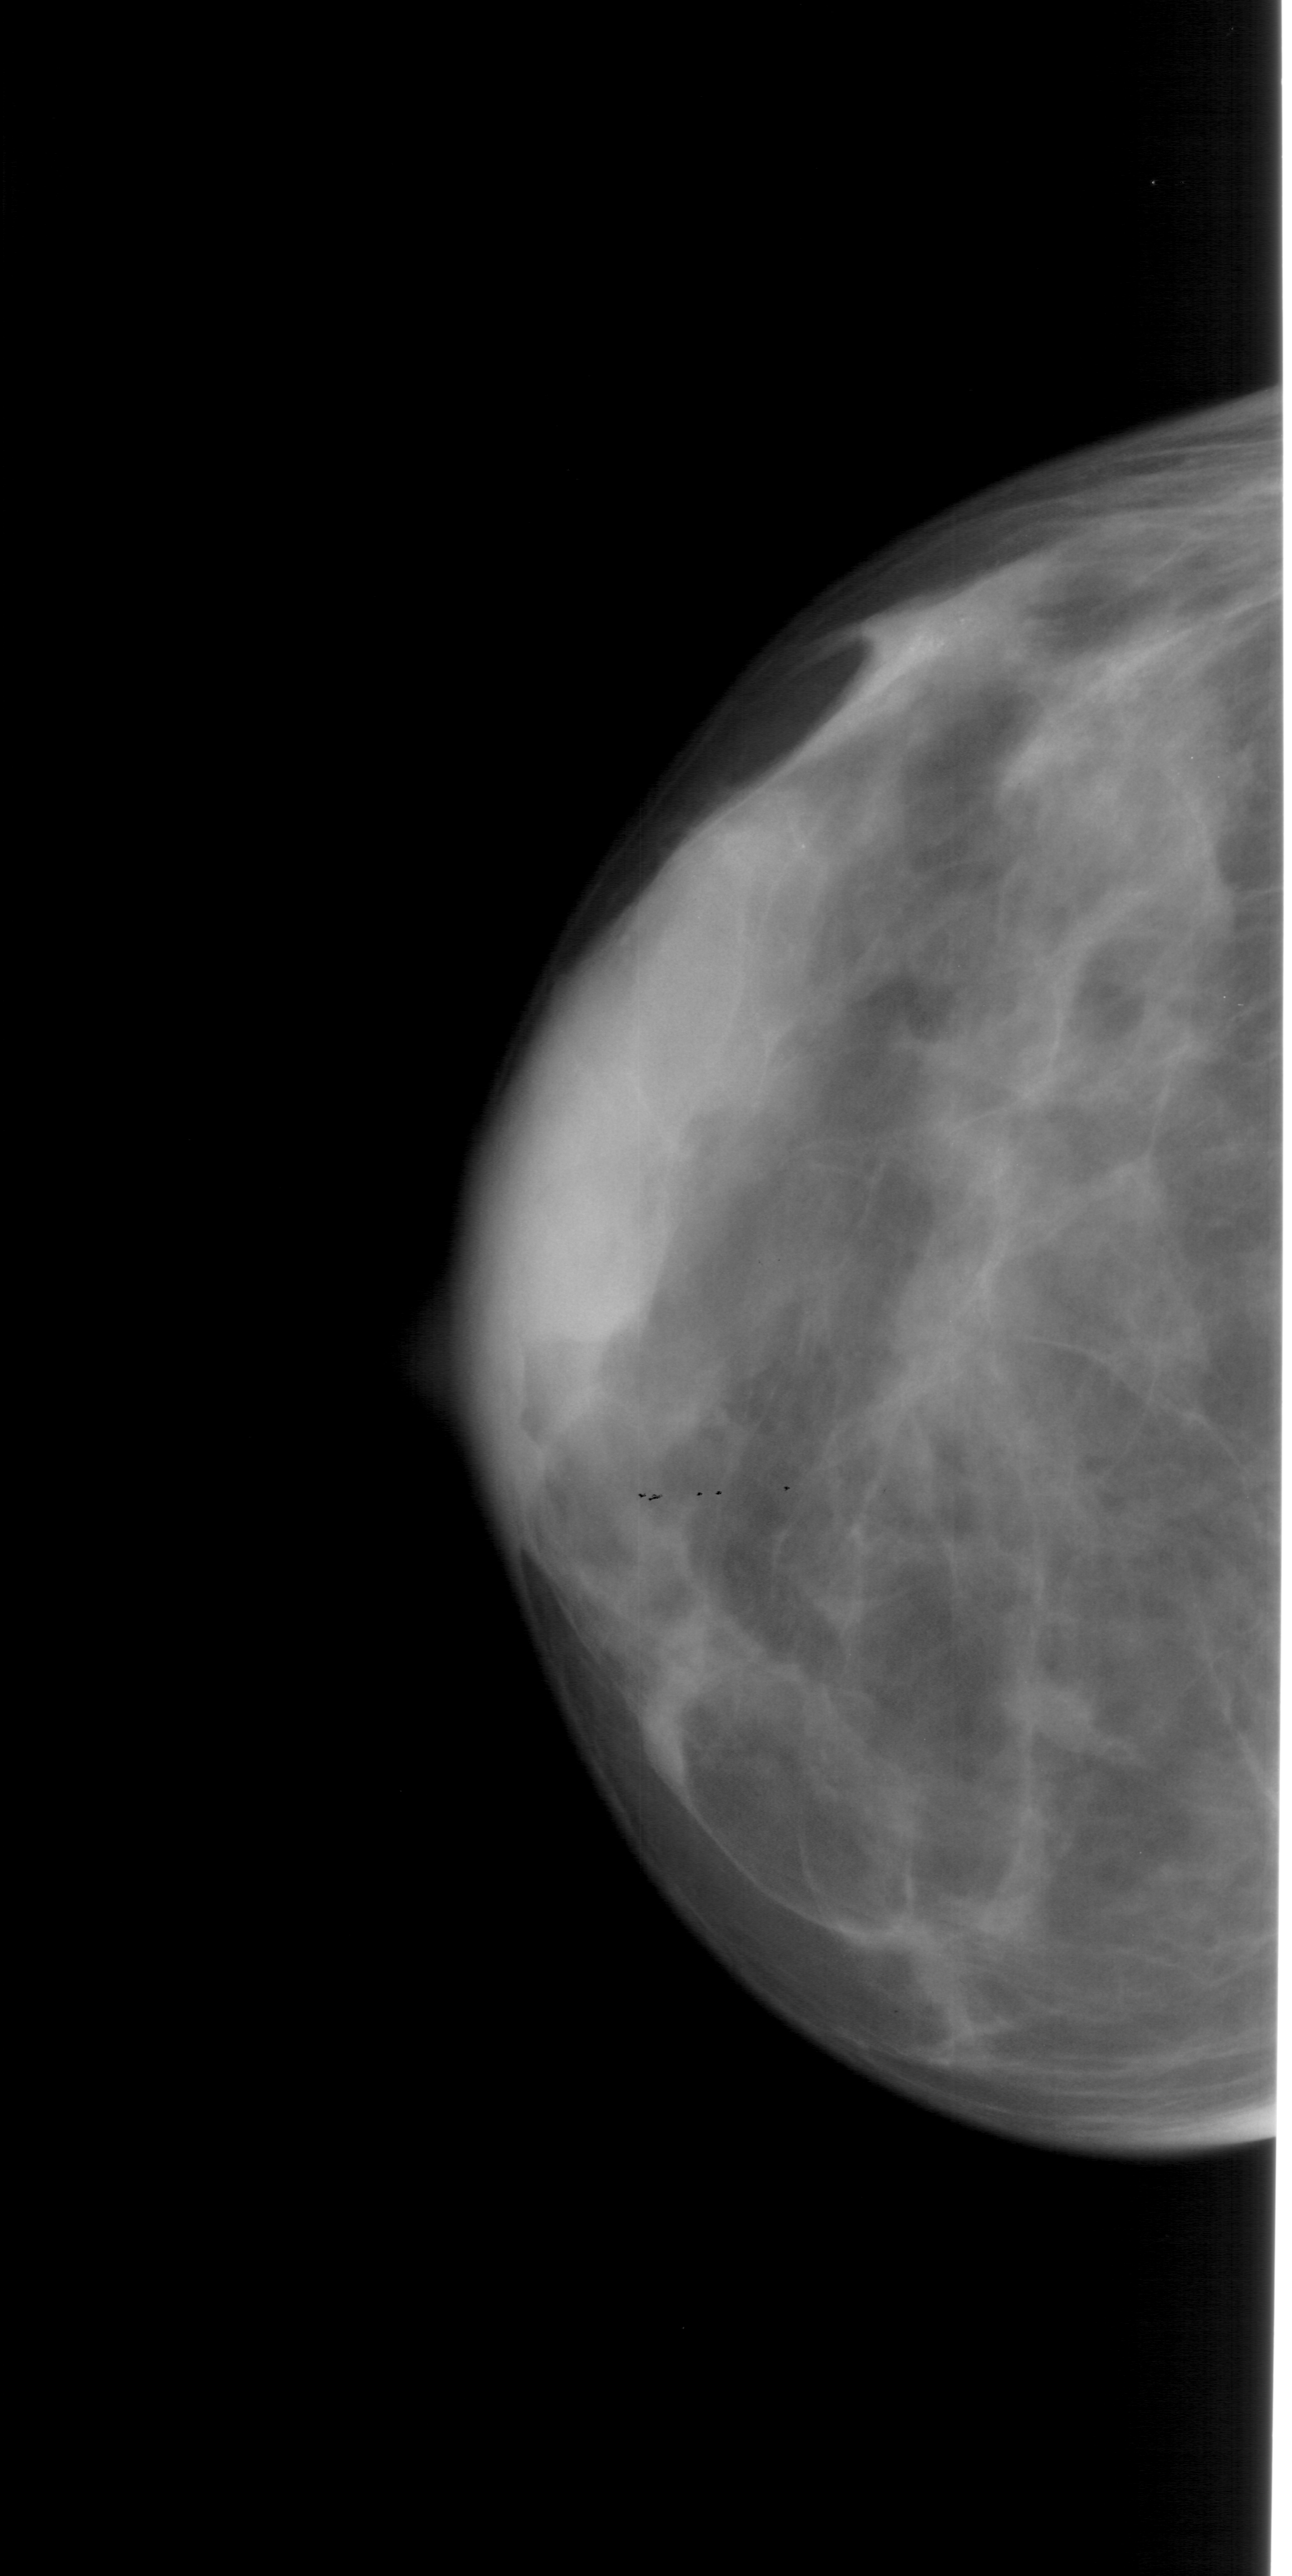
Scanned film-screen mammogram, left breast, craniocaudal (CC) view, BI-RADS breast density category 4 (scale 1–4).
Calcifications, morphology pleomorphic, distribution clustered; BI-RADS assessment category 4; subtlety rating 1 on a 1 (subtle) to 5 (obvious) scale; pathology (as recorded): benign.